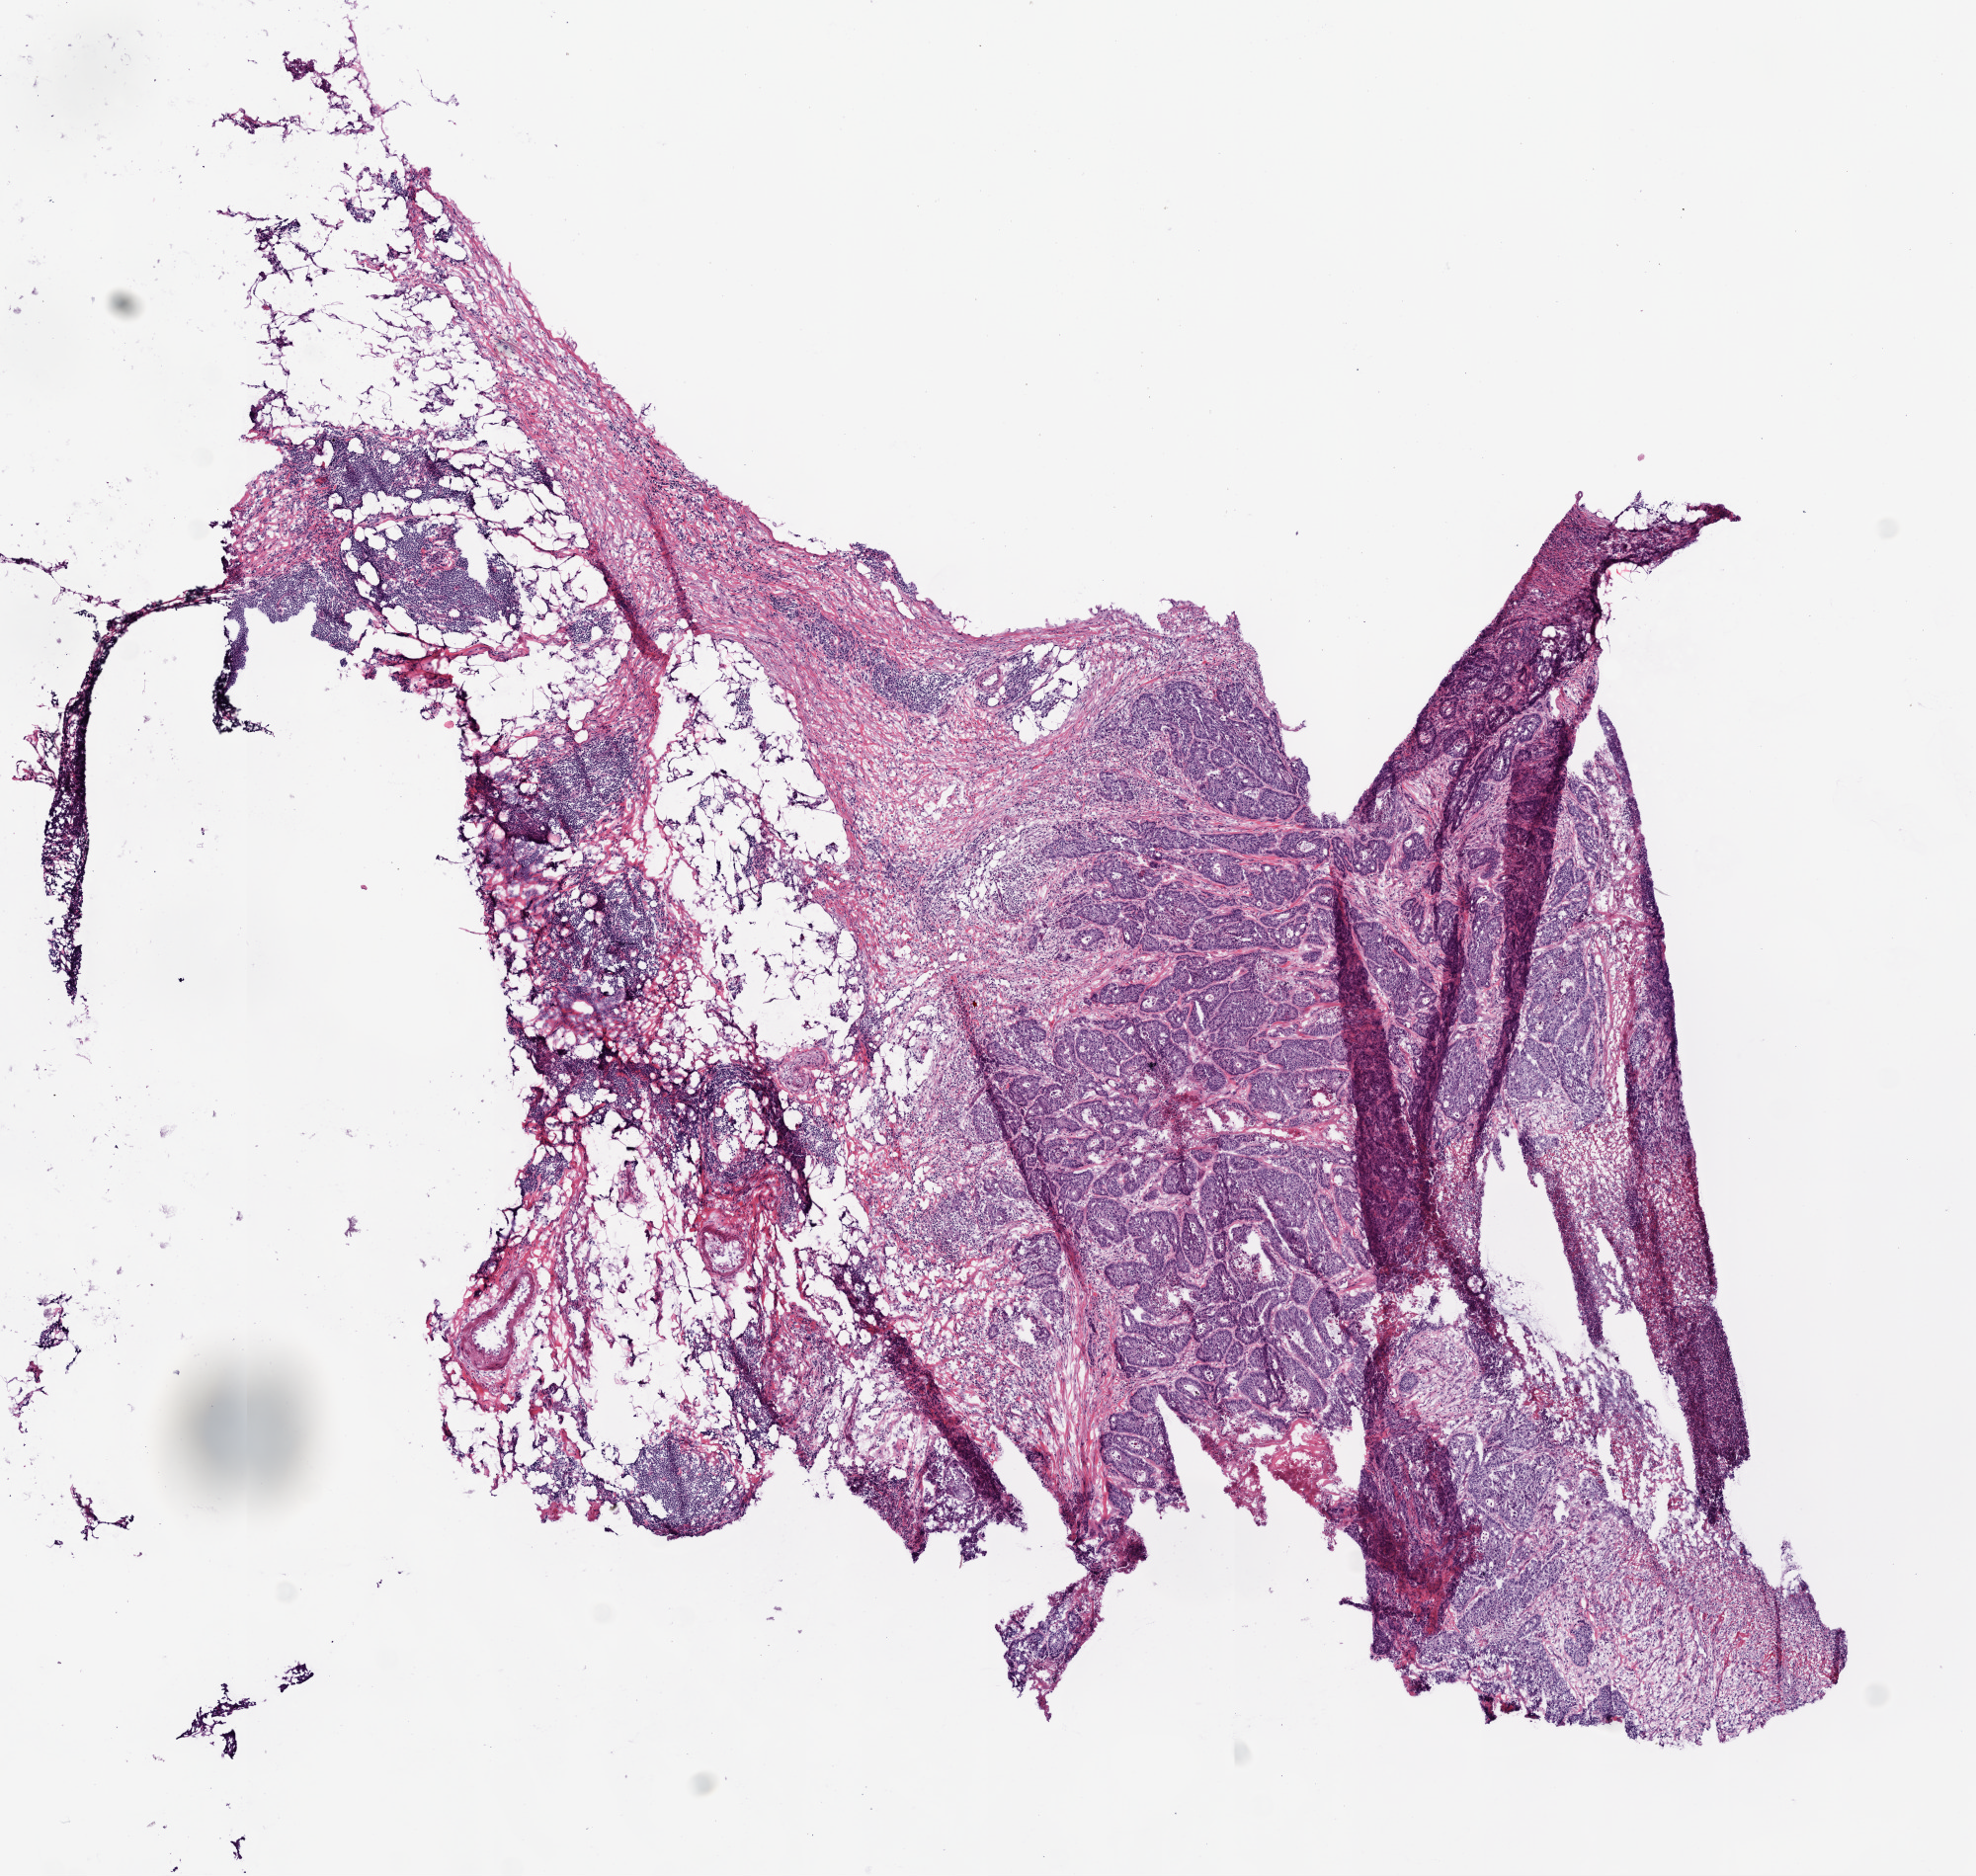
Whole-slide histology image, Hematoxylin and eosin (H&E) stained — a low-resolution overview of the entire scanned area, about 8.0 x 7.6 mm (slide scanned at 20x), frozen section, primary tumour sample from the colon. Male patient; age at initial diagnosis 75 years. Pathologist review of this section (percent, as recorded): tumour cells 52%, tumour nuclei 60%, normal cells 30%, stromal cells 10%, necrosis 8%. Infiltration values recorded for this section: lymphocyte infiltration 30%.
Pathologic diagnosis: Adenocarcinoma, NOS. AJCC pathologic stage: II (5th edition).